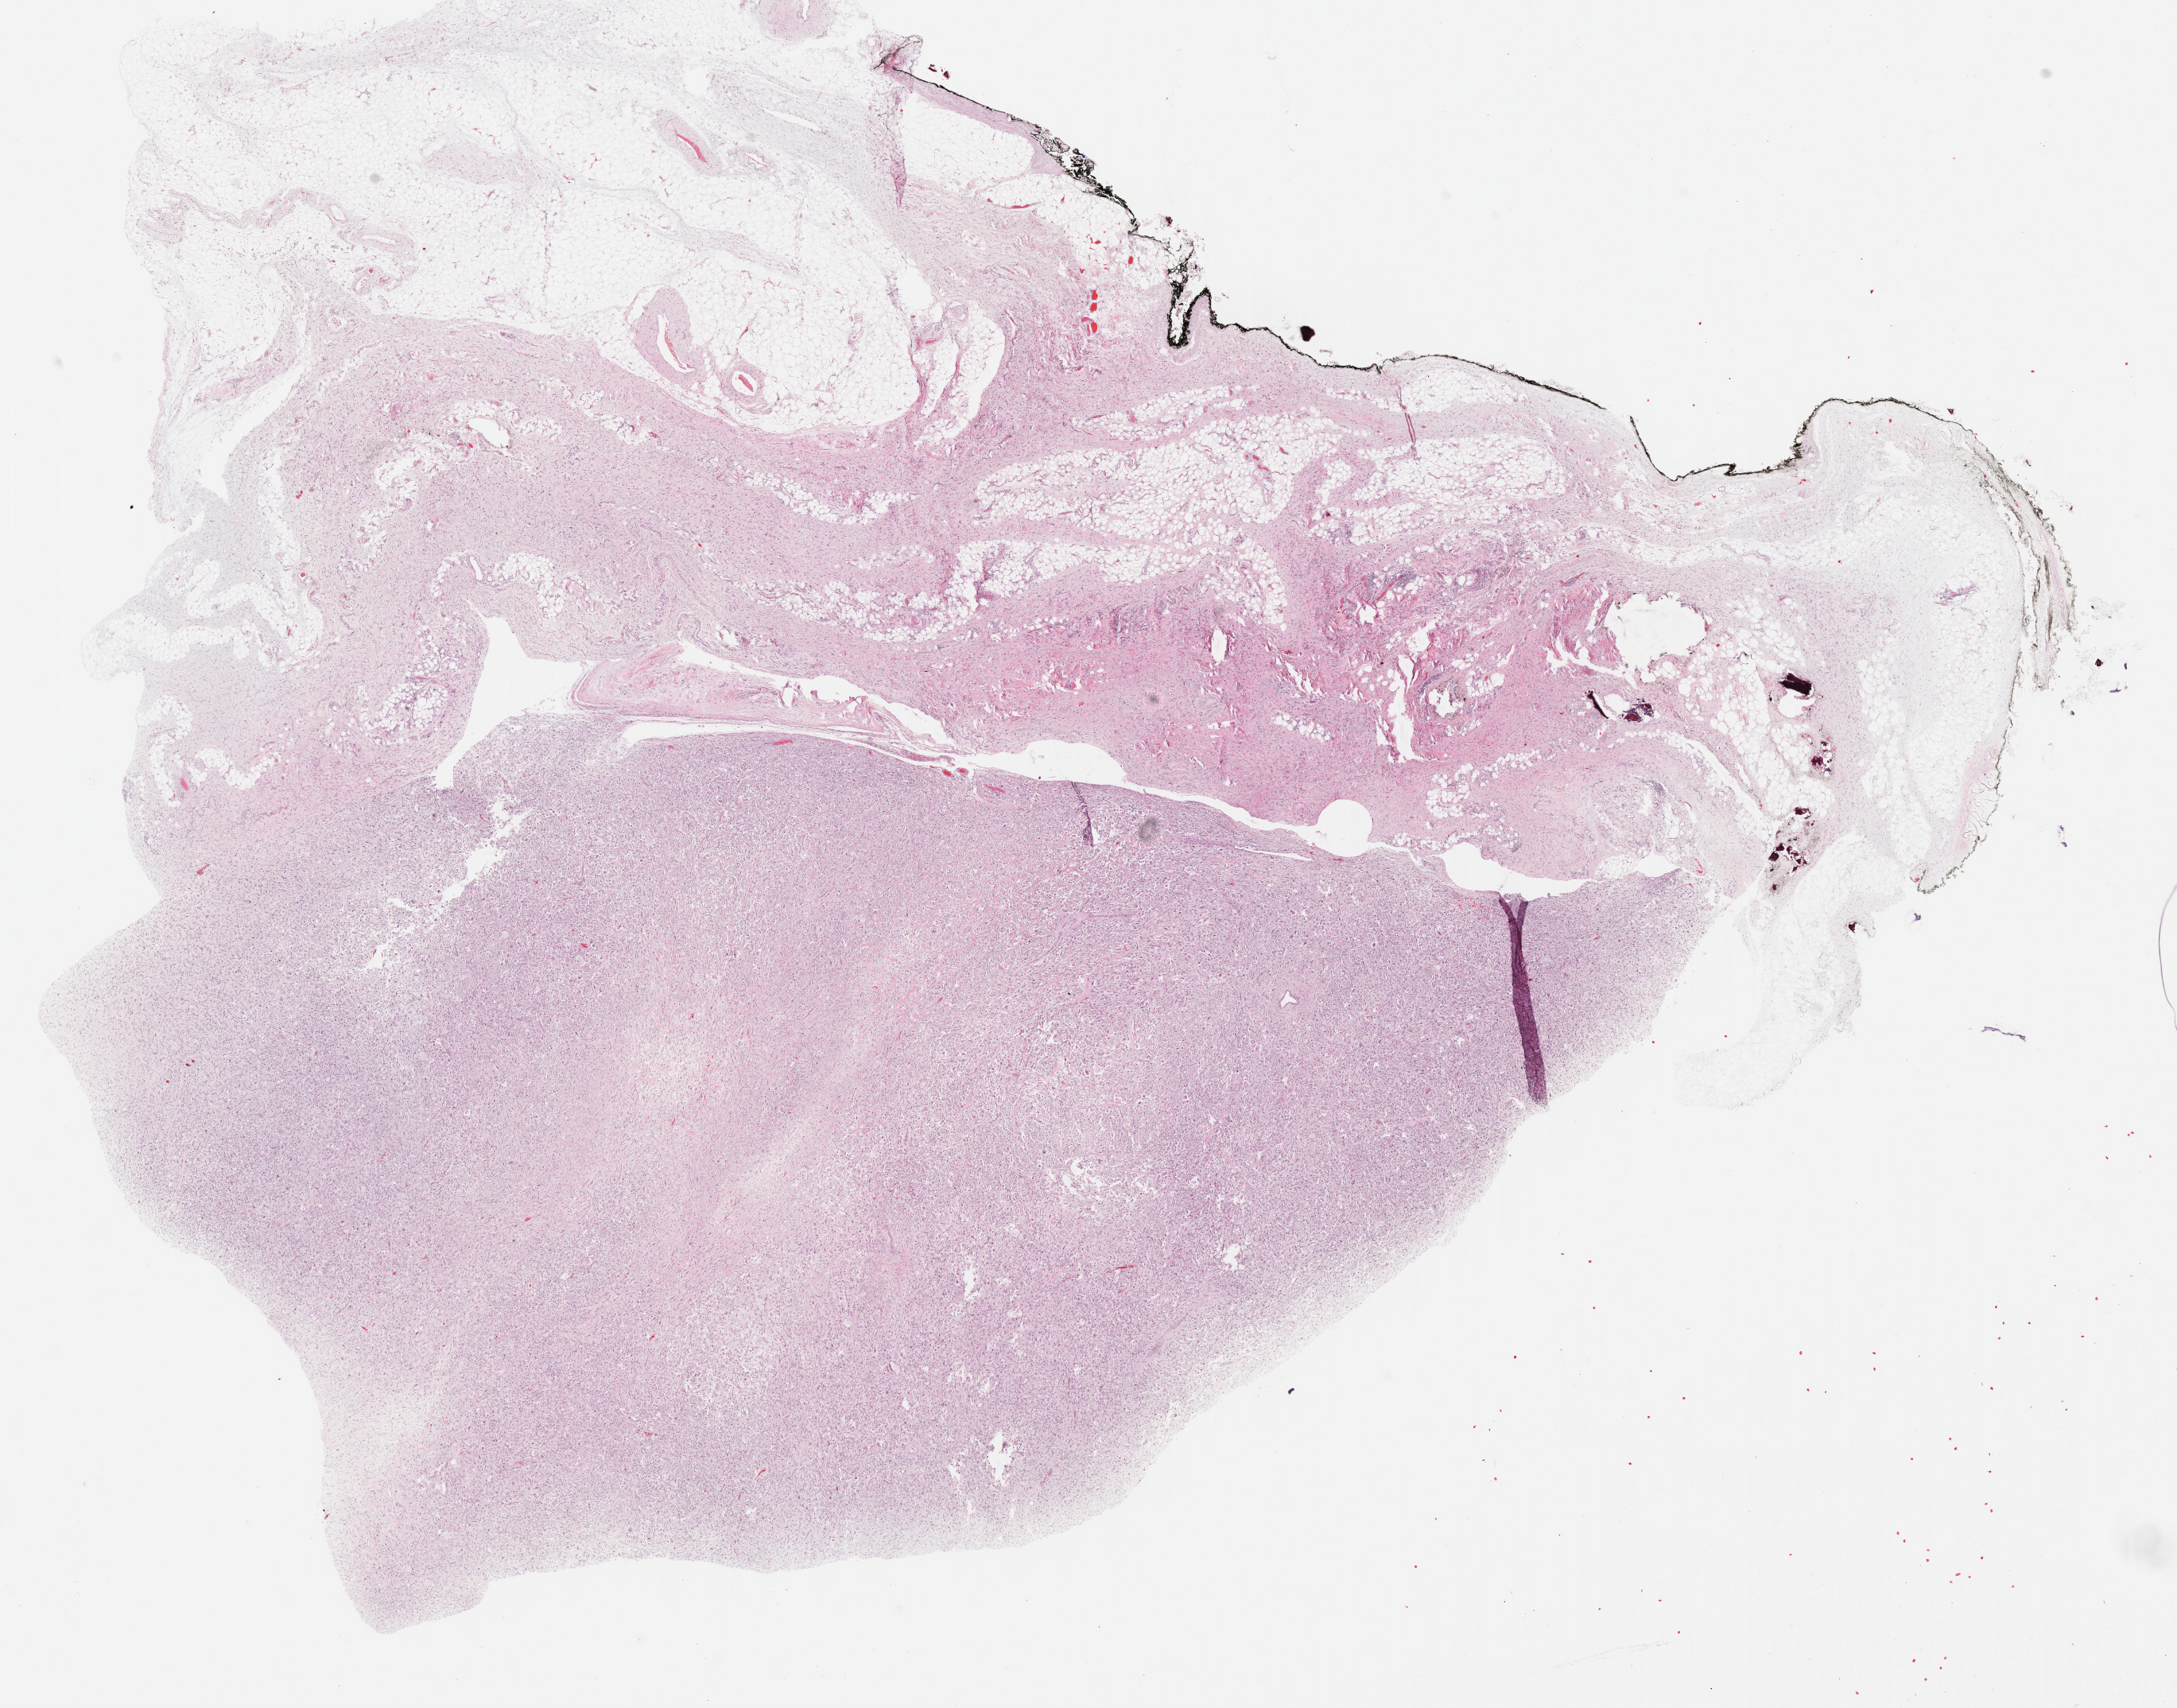
Digitized H&E-stained tissue section (whole slide), whole scanned area (about 22.1 x 17.4 mm, acquisition: 40x scan) shown as a low-resolution overview. FFPE section. Primary tumour sample from the connective, subcutaneous and other soft tissues. Patient sex: male.
- histologic diagnosis: Dedifferentiated liposarcoma (connective, subcutaneous and other soft tissues of thorax)